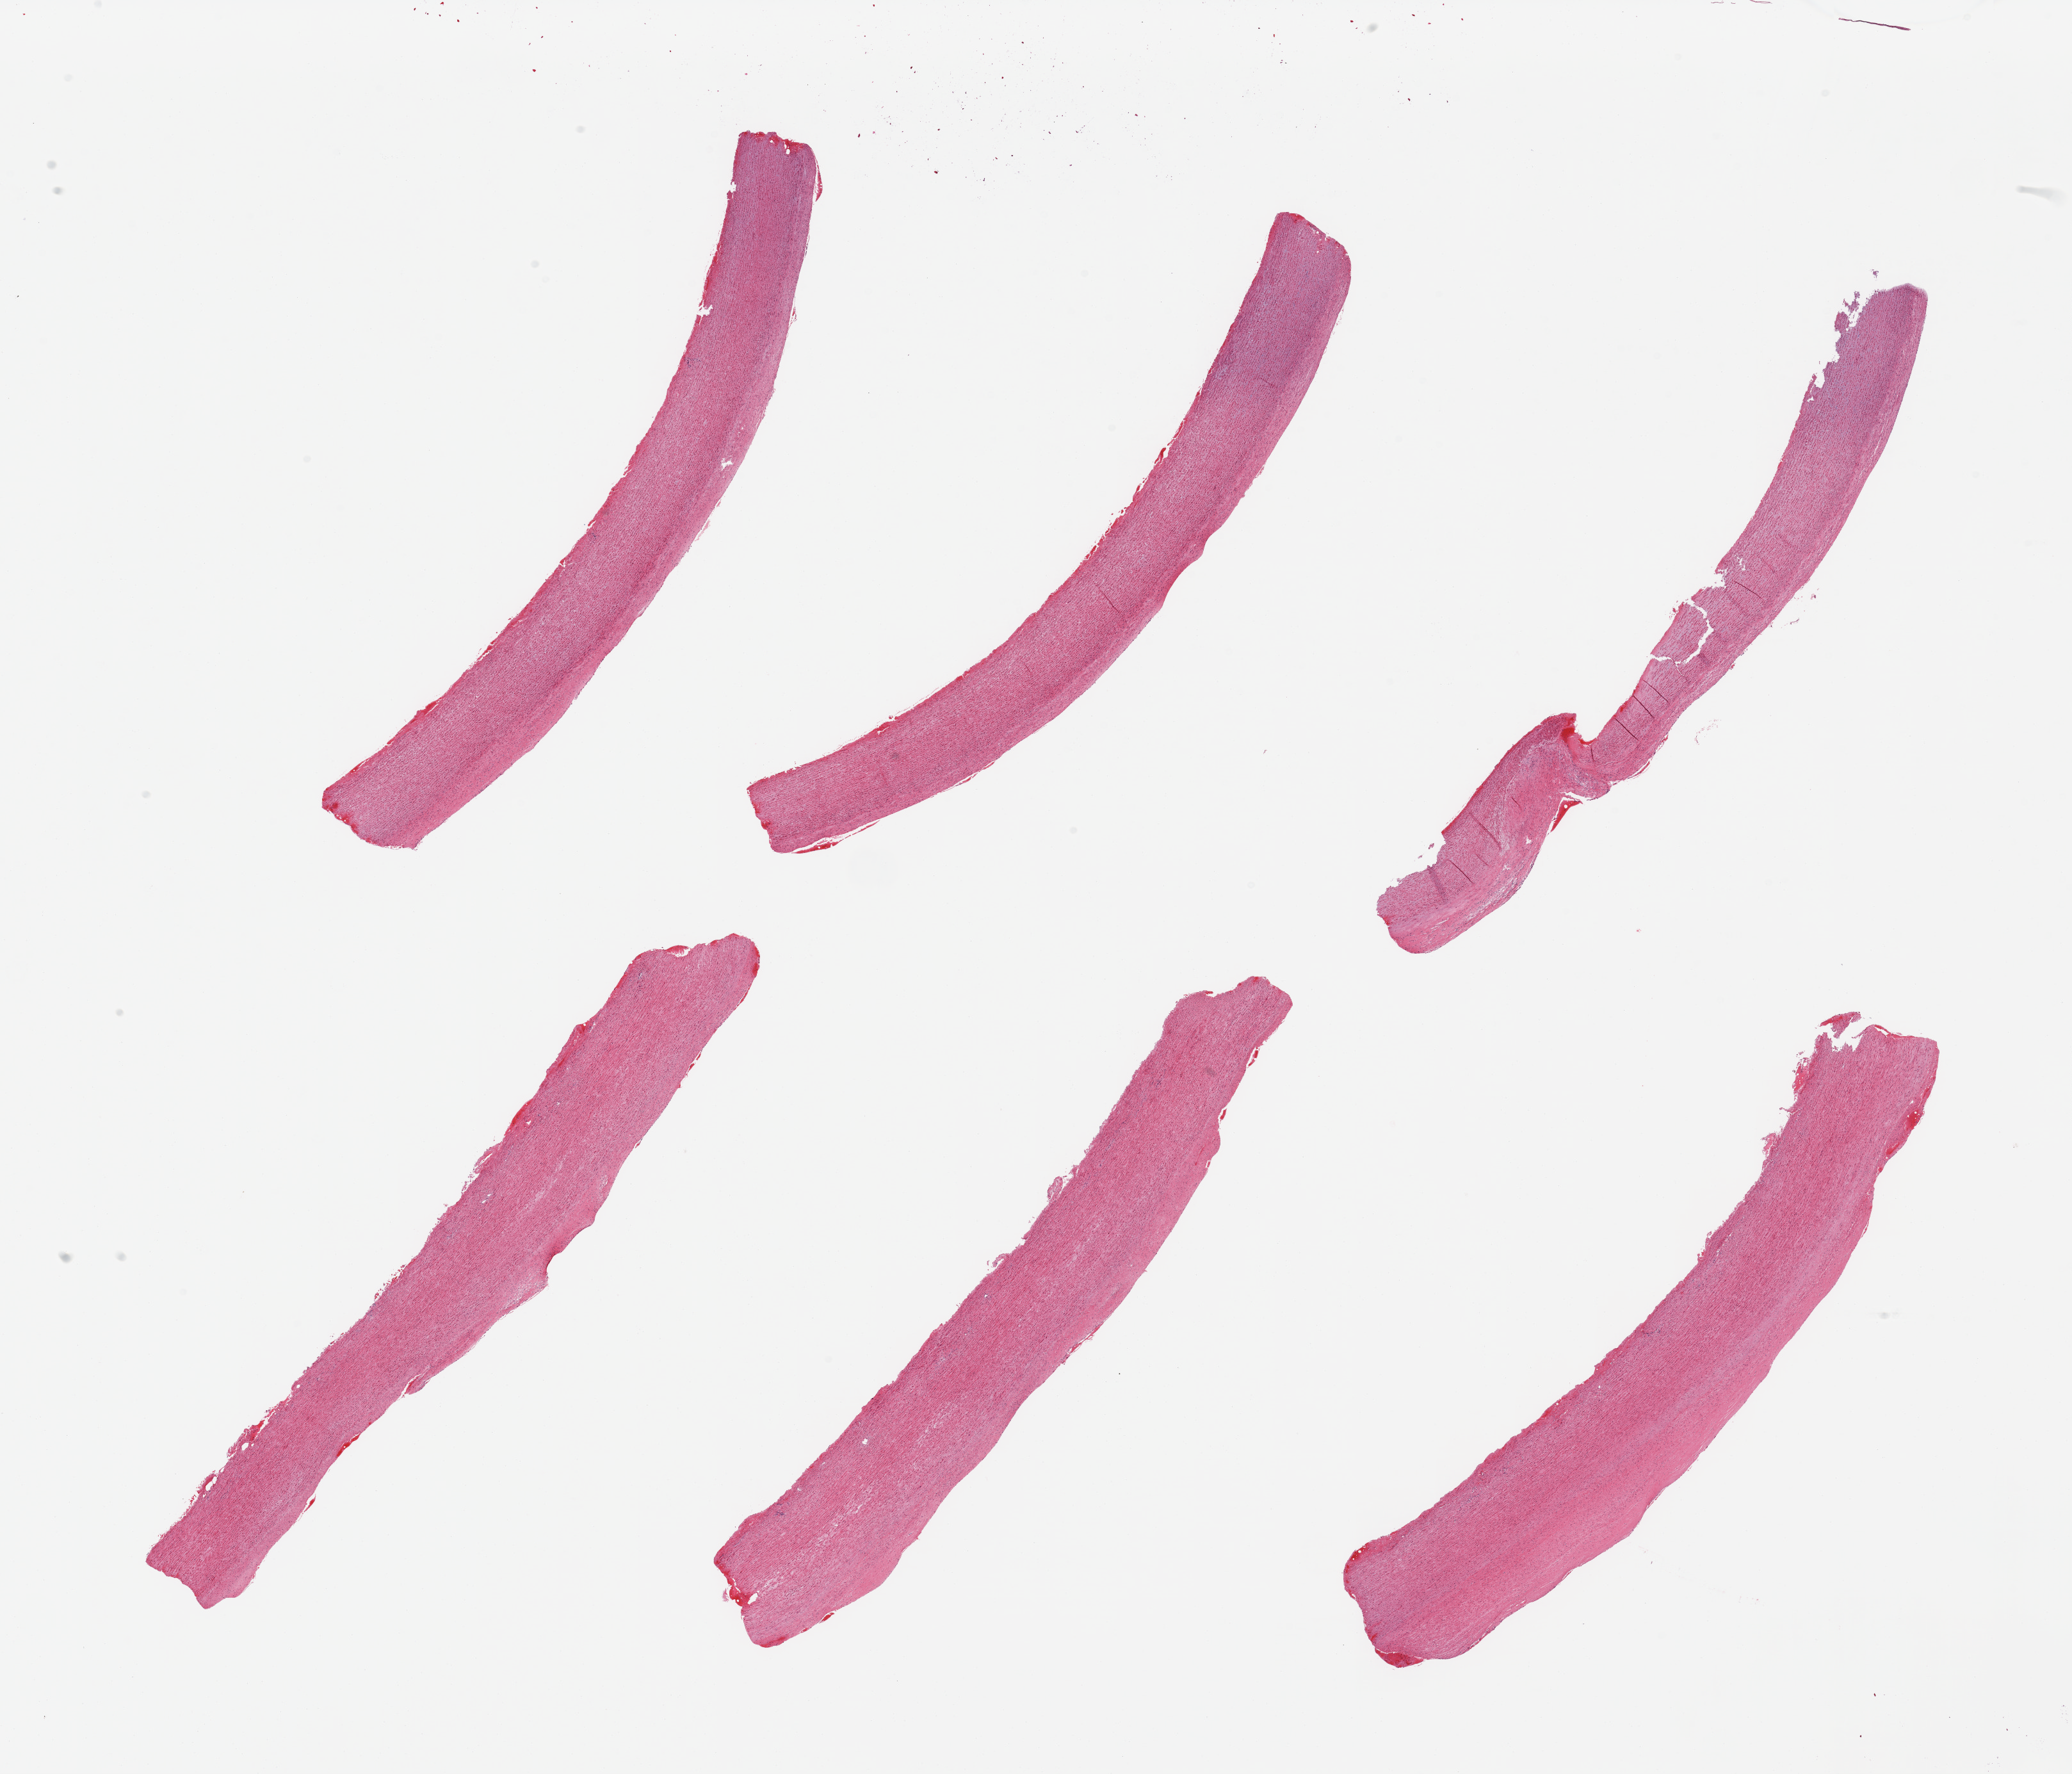
Whole-slide image, H&E stain, brightfield — whole scanned area (about 25.6 x 21.9 mm) shown as a low-resolution overview; PAXgene-fixed paraffin-embedded (PFPE) section; section of aorta (target tissue); donor tissue sample. Donor sex: male.
• review note (as recorded): 6 pieces; atherosclerosis